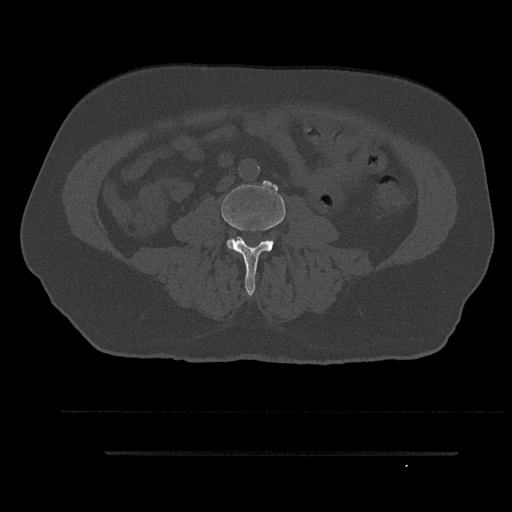
CT including the spine, one axial slice. Position 26 of 797 along the scan axis. Reconstruction kernel Br40s/3. 120 kVp. Bone window (W 1800 / L 400 HU). 512 × 512 image matrix, field of view 432 × 432 mm. Patient: male, 63 years. Case-level facts recorded for this patient, not image findings: primary cancer: renal.
Outlined on this slice (semi-automatically segmented with operator editing):
- L3 vertebra: box from (x=221, y=185) to (x=285, y=296) px
- L4 vertebra: (x=267, y=240)–(x=274, y=250)